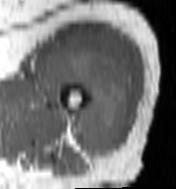
MRI of an extremity soft-tissue mass, one axial slice; position 74 of 100 along the scan axis; MR volume resampled by the dataset authors to the PET/CT grid (not the native acquisition matrix); 3.27 mm slice thickness; 176 × 189 image matrix, field of view 172 × 185 mm. Female patient. Case-level facts recorded for this patient, not image findings: histological type: undifferentiated – high grade; grade: high; site of the primary tumour: left thigh.
Outlined on this slice (expert contour drawn on MRI and transferred to this co-registered scan by the dataset authors):
- gross tumour volume including surrounding oedema: bounding box <44,34,134,158> (left, top, right, bottom; pixels)
- gross tumour volume (mass): <46,34,134,158>